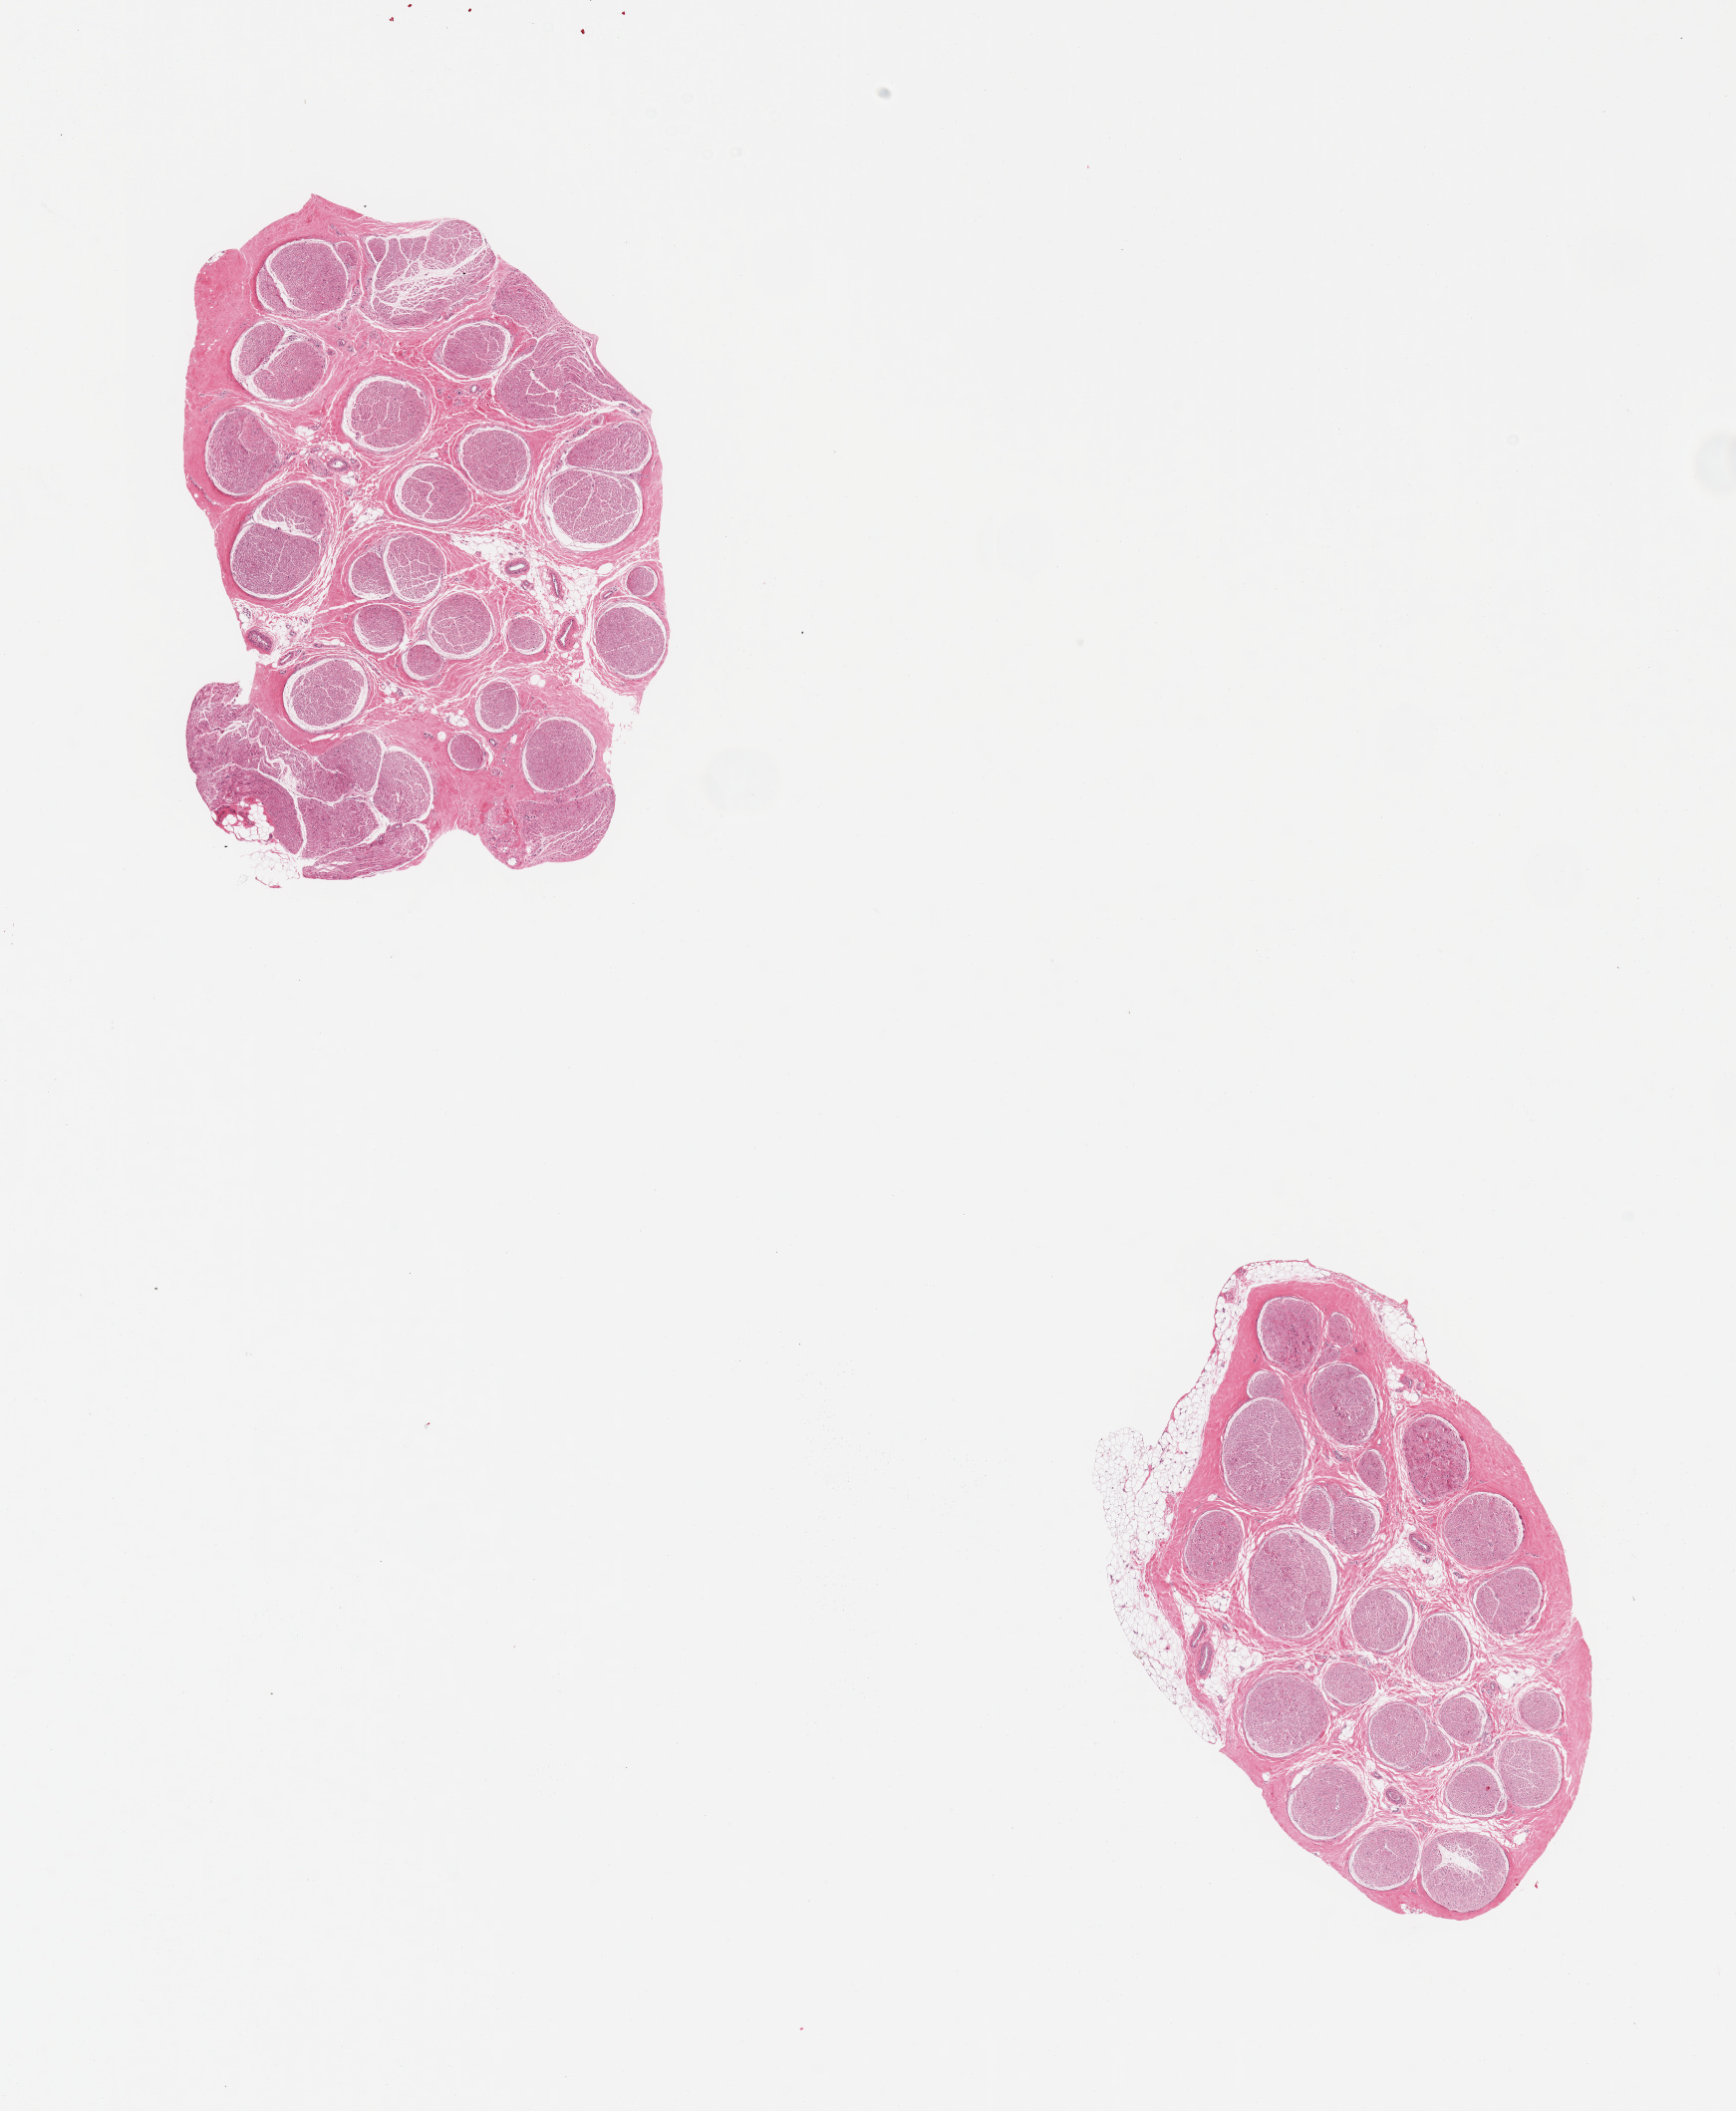
Digitized haematoxylin and eosin-stained section, brightfield, a low-resolution overview of the entire scanned area, about 13.8 x 16.8 mm. PAXgene-fixed, paraffin-embedded tissue. Target tissue: tibial nerve. Tissue donor sample. Donor sex: male.
Pathologist's review note for this sample: 2 pieces; not artery, sections of nerve with trace and ~5% of external fat.